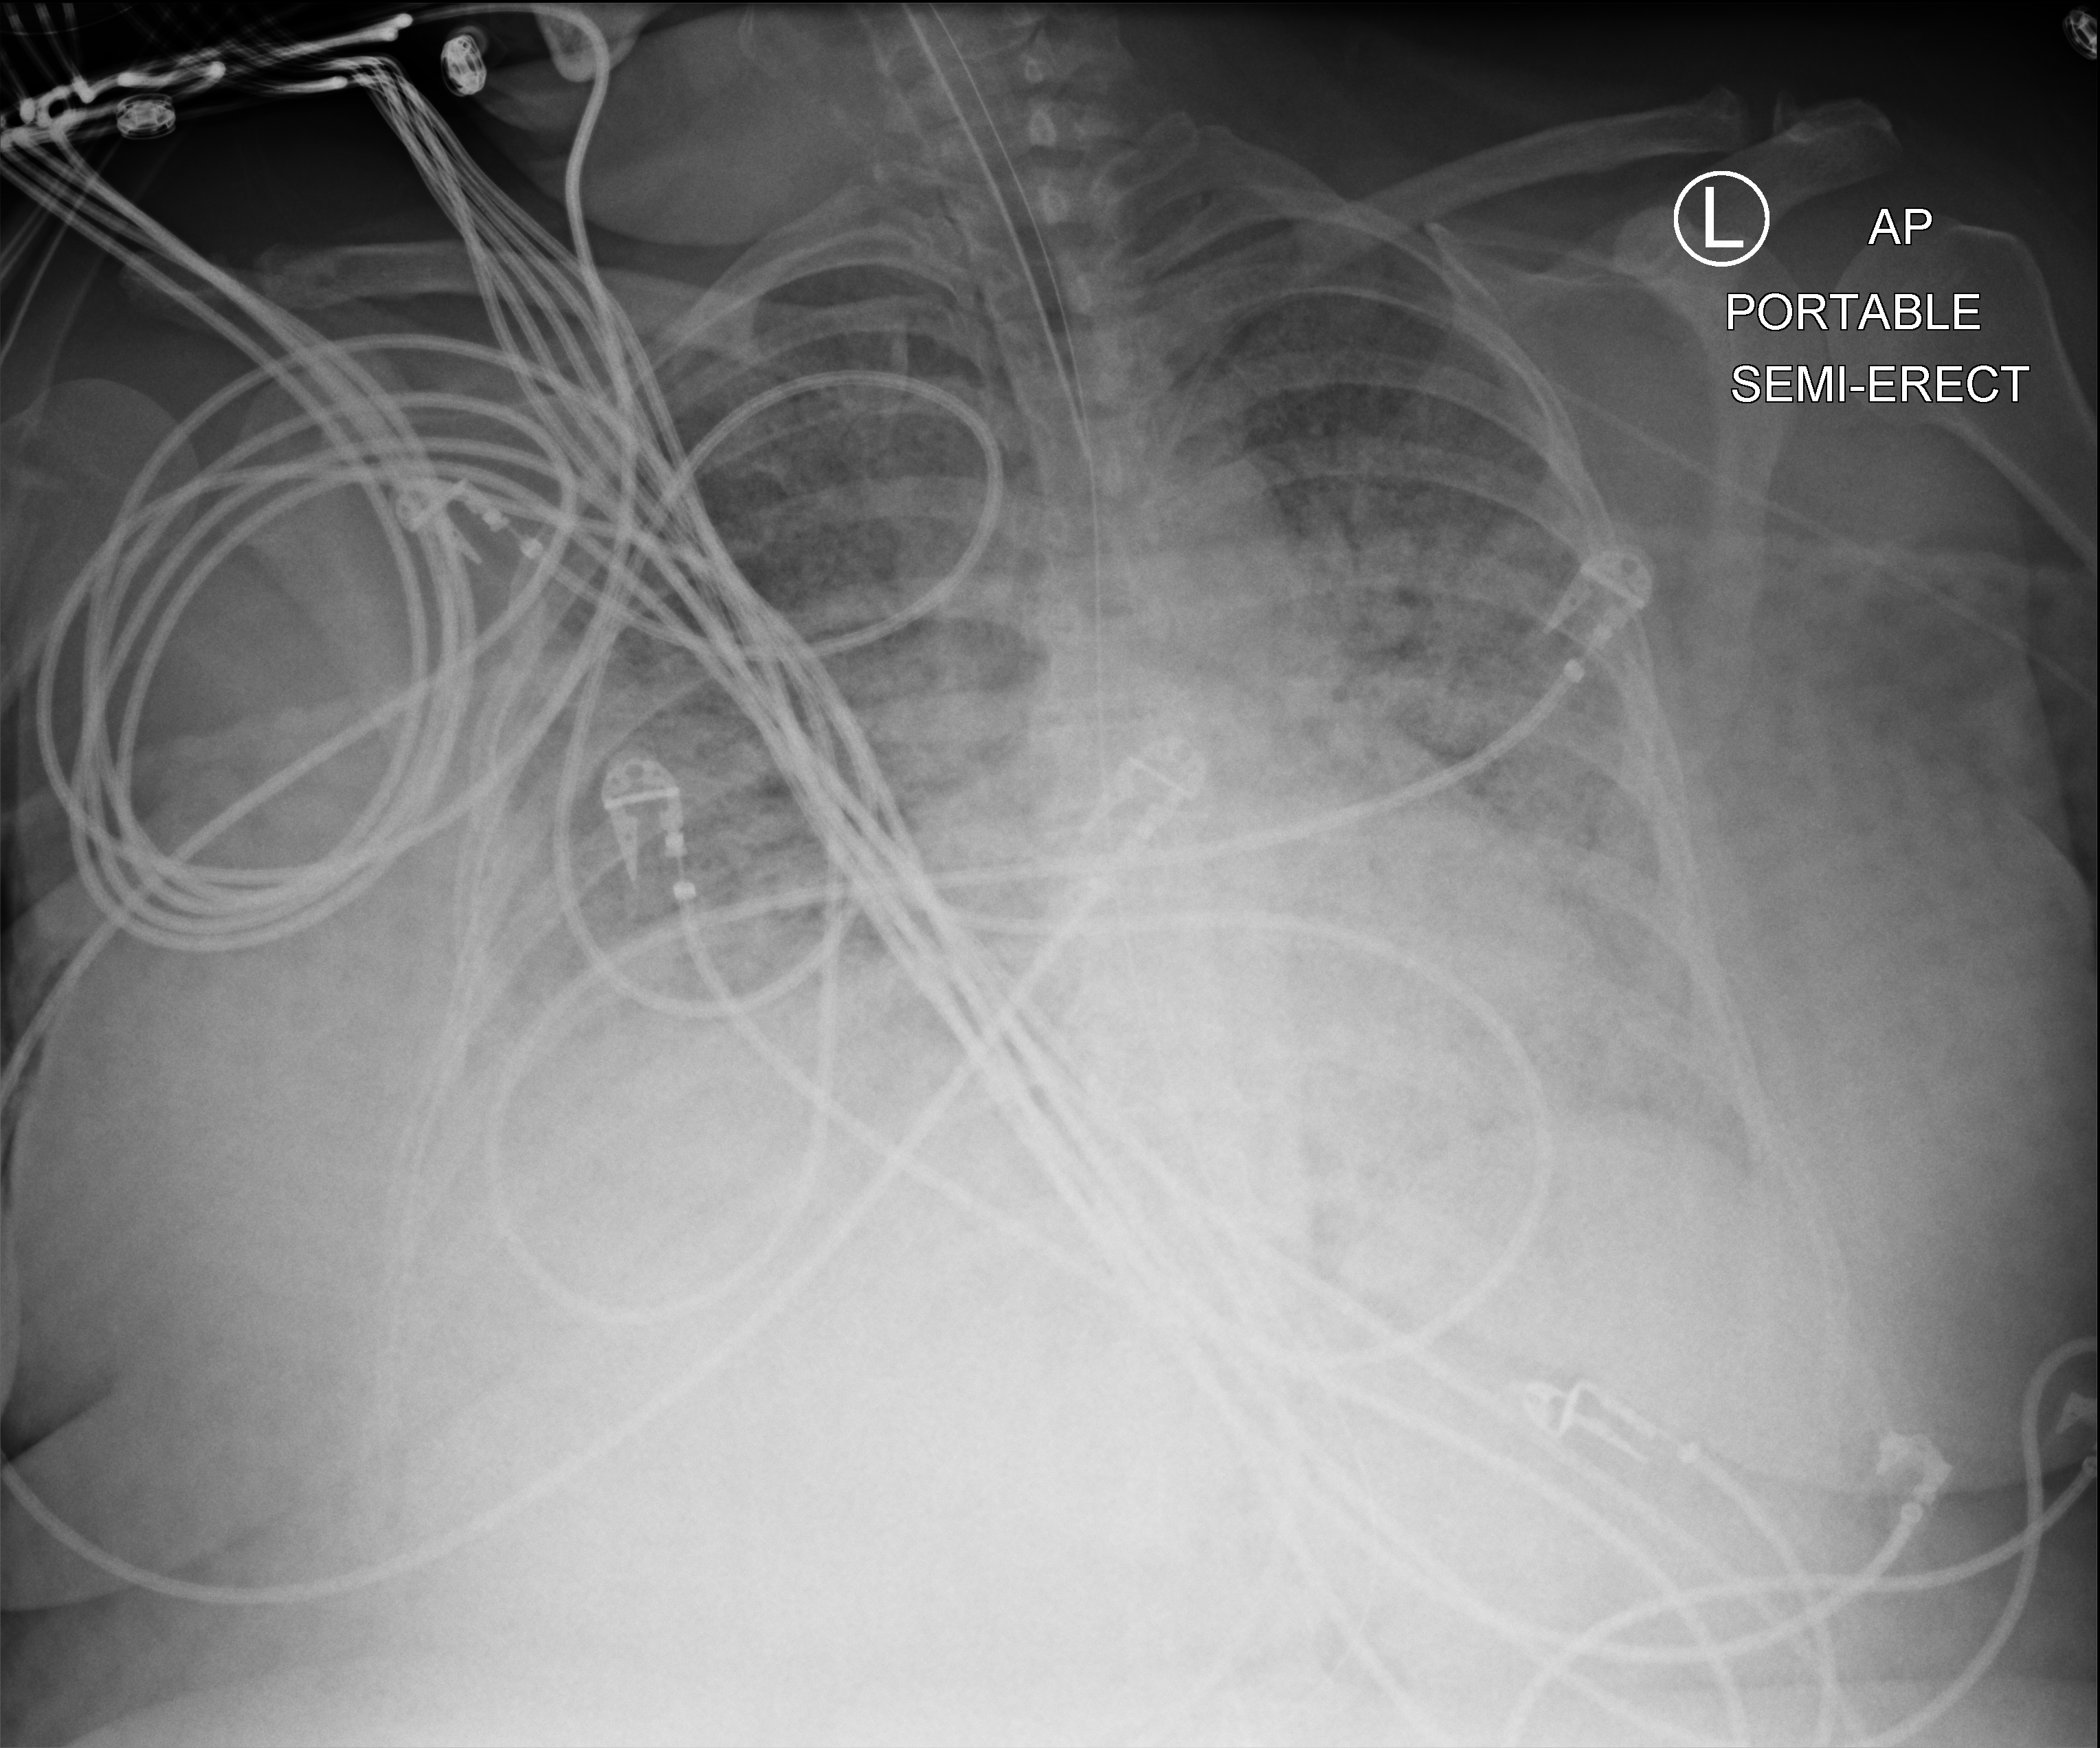
Bedside chest radiograph (computed radiography), anteroposterior (AP) projection. Patient hospitalised with COVID-19; female, aged 18–59 years.
Hospital-stay facts (about this admission, not read from this image; timing relative to this image not recorded): length of hospital stay: 95 days.